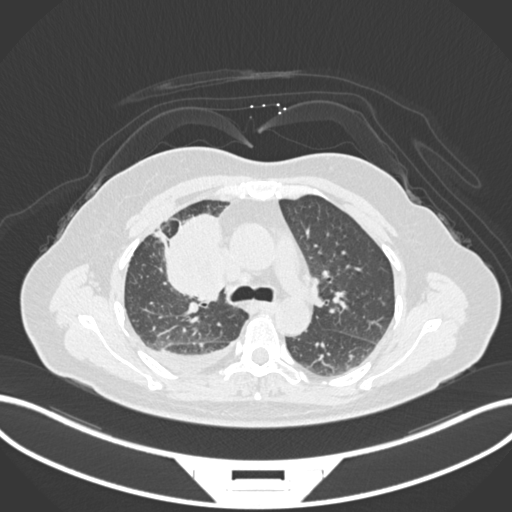
Chest CT, one axial slice; slice 99 of 172 in the series (ordered by position); reconstruction kernel B30f; 120 kVp; lung window (W 1500 / L -600 HU); 512 × 512 image matrix, field of view 400 × 400 mm. Female patient, age 52 years. From the clinical record (not read from this slice): clinical TNM (as recorded): T3 N1 M1.
Structures marked on this image (rectangle marked by the reading radiologist):
- lung tumour (recorded histology: adenocarcinoma): bounding box (x1, y1, x2, y2) in pixels: (149, 211, 230, 304)